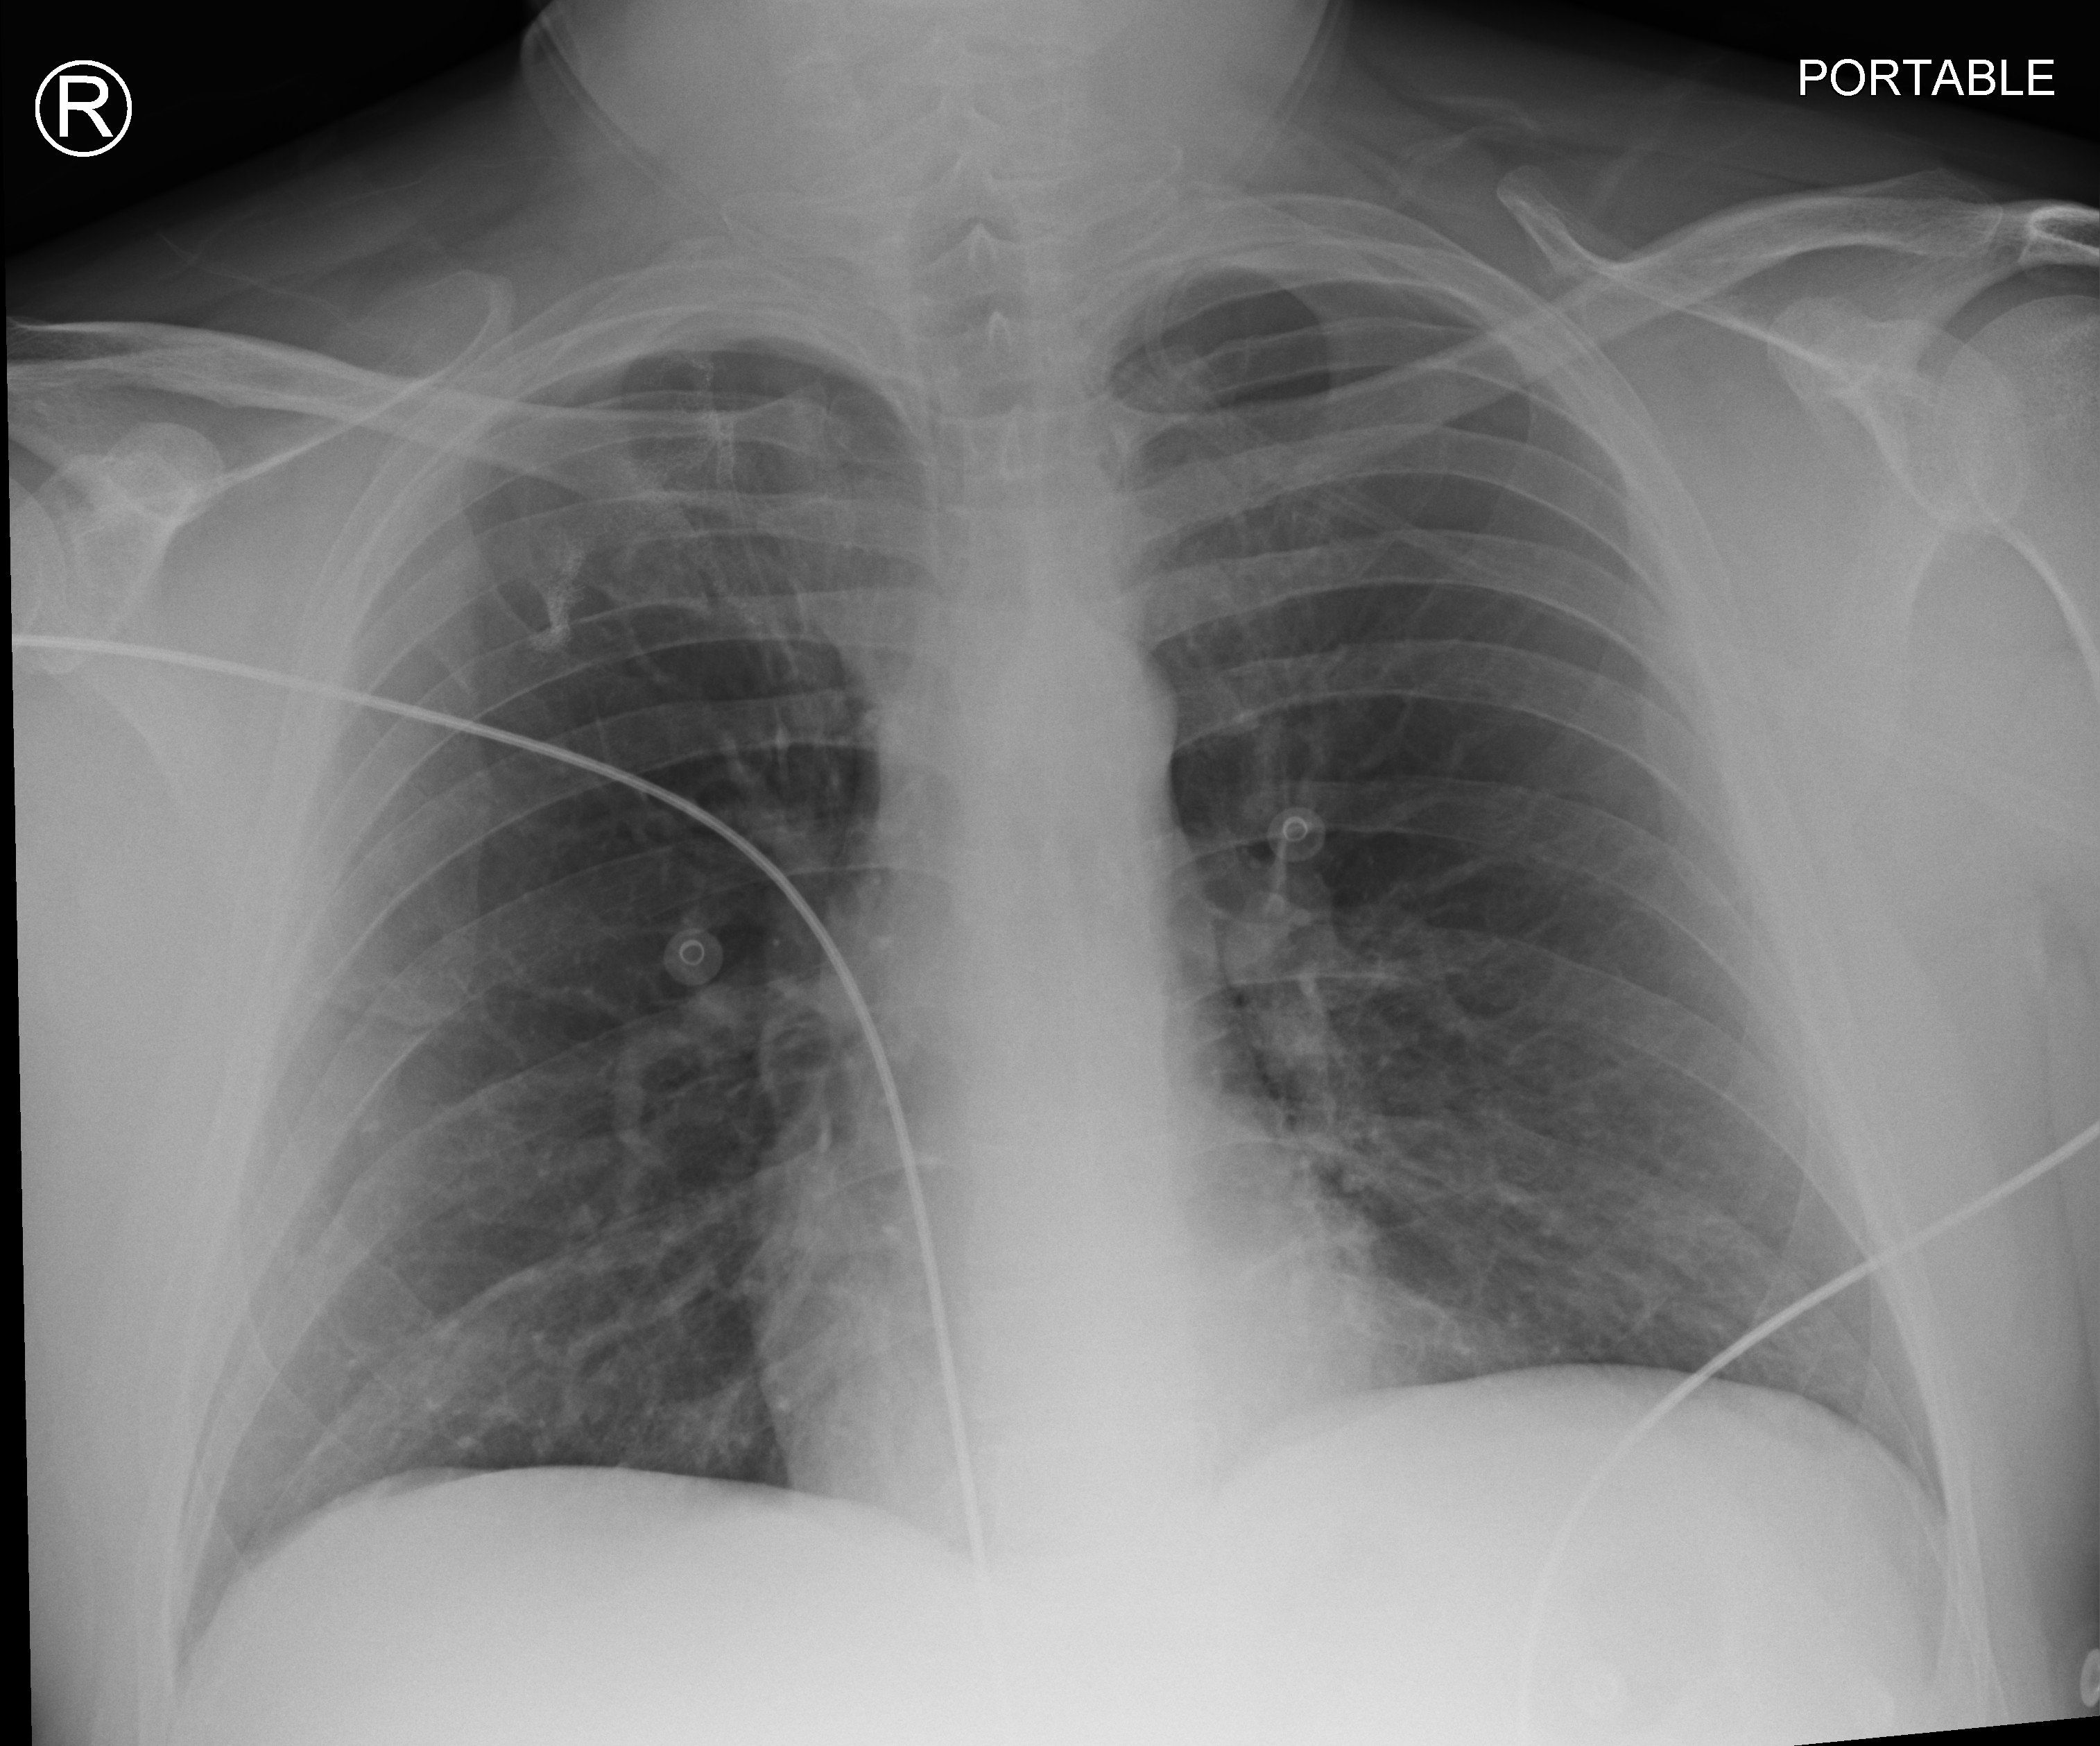
Bedside chest radiograph (computed radiography). Male patient hospitalised with COVID-19, age 18–59 years.
Admission-level facts for this patient (not findings on this image; timing relative to this image not recorded): mechanically ventilated during this hospital stay: no; admitted to intensive care during this hospital stay: no.